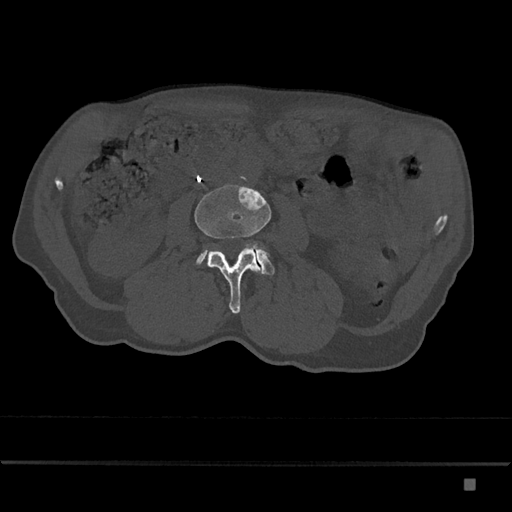
CT including the spine, one axial slice; bone window (W 1800 / L 400 HU); 0.5 mm slice thickness; 512 × 512 image matrix, field of view 390 × 390 mm. Patient: male, 72 years. From the clinical record (not read from this slice): primary cancer: prostate.
Annotated regions visible in this slice (semi-automatic segmentation, software-assisted and operator-edited):
- L3 vertebra: box from (x=194, y=184) to (x=272, y=314) px
- L4 vertebra: (x=197, y=244)–(x=275, y=275)